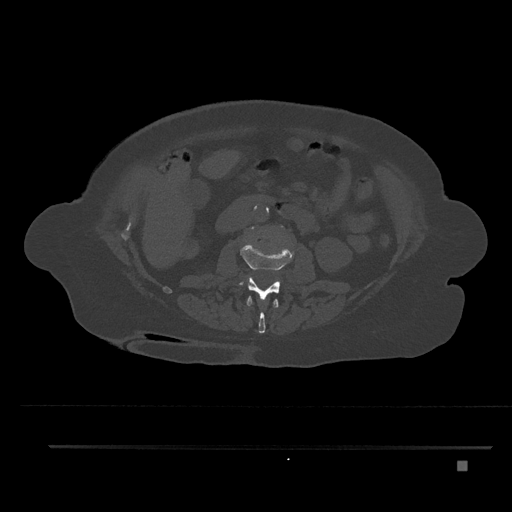
CT including the spine, one axial slice. Slice 172 of 797 in the series (ordered by position). 120 kVp. Bone window (W 1800 / L 400 HU). 0.5 mm slice thickness. 512 × 512 image matrix. Patient: female, 76 years. Case-level facts recorded for this patient, not image findings: primary cancer: lung.
Outlined on this slice (semi-automatic segmentation, software-assisted and operator-edited):
- L1 vertebra: box from (x=246, y=296) to (x=279, y=334) px
- L2 vertebra: (x=234, y=244)–(x=304, y=303)
- L3 vertebra: (x=248, y=229)–(x=278, y=278)